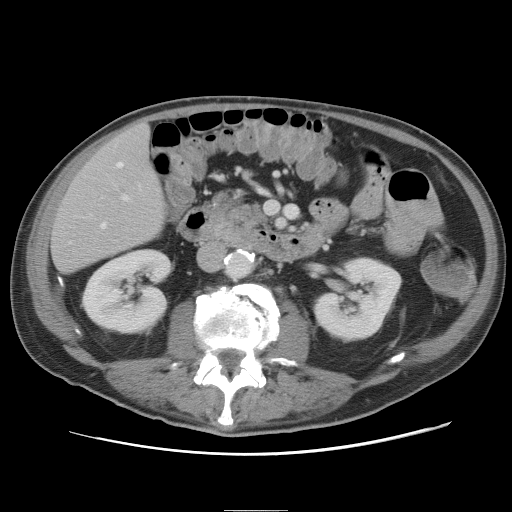
Contrast-enhanced abdominal CT, one axial slice; slice 20 of 89 in the series (ordered by position); intravenous contrast given; soft-tissue window (W 400 / L 40 HU); 5 mm slice thickness; 512 × 512 image matrix, field of view 375 × 375 mm. Male patient, age 69 years. Case-level facts recorded for this patient, not image findings: diagnosis: colorectal cancer liver metastases, imaged before liver resection; multiple liver metastases: no; largest metastasis: 8.5 cm.
Annotated regions visible in this slice (manually delineated by an expert):
- hepatic veins: bounding box (x1, y1, x2, y2) in pixels: (102, 162, 123, 228)
- liver: (52, 125, 165, 273)
- planned liver remnant (the part of the liver to remain after resection): (53, 125, 166, 272)
- portal vein (with intrahepatic branches): (122, 195, 130, 201)